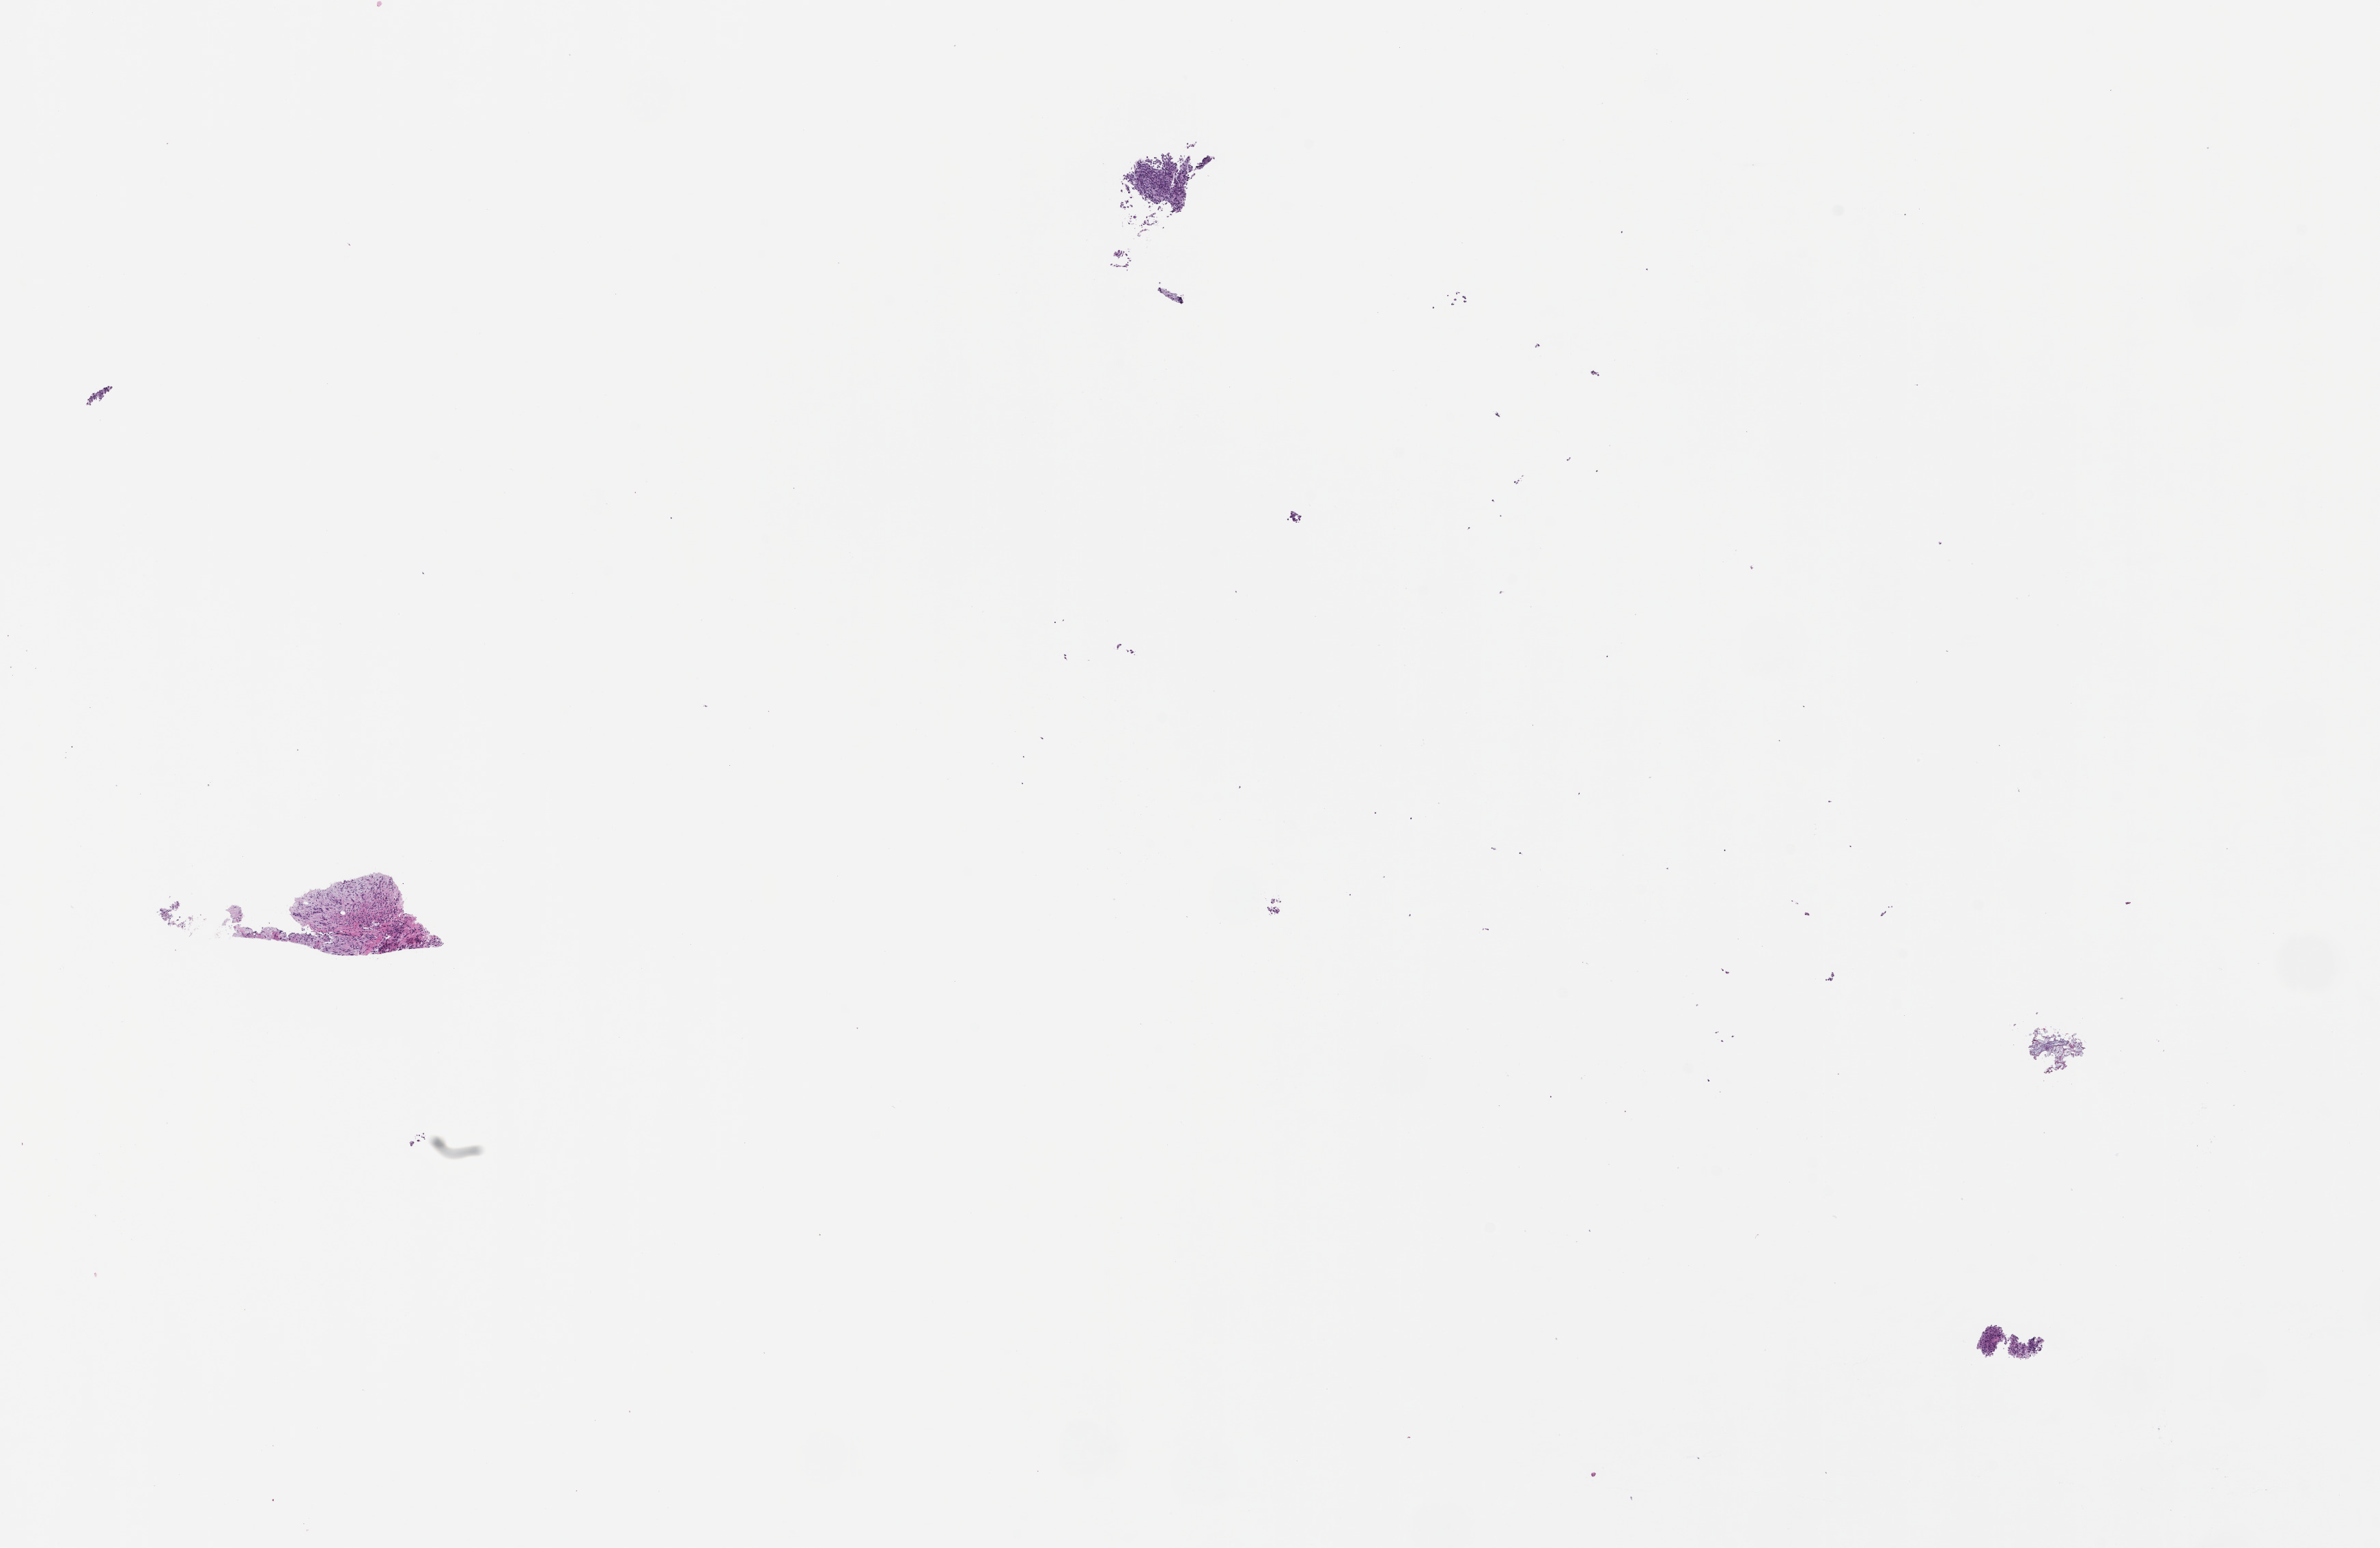
Whole-slide image, H&E stain — shown as a low-resolution overview of the whole scanned area (about 14.1 x 9.1 mm). Formalin-fixed paraffin-embedded section. Patient sex: female.
- this section: metastatic tumor tissue
- primary diagnosis of the patient: Melanoma